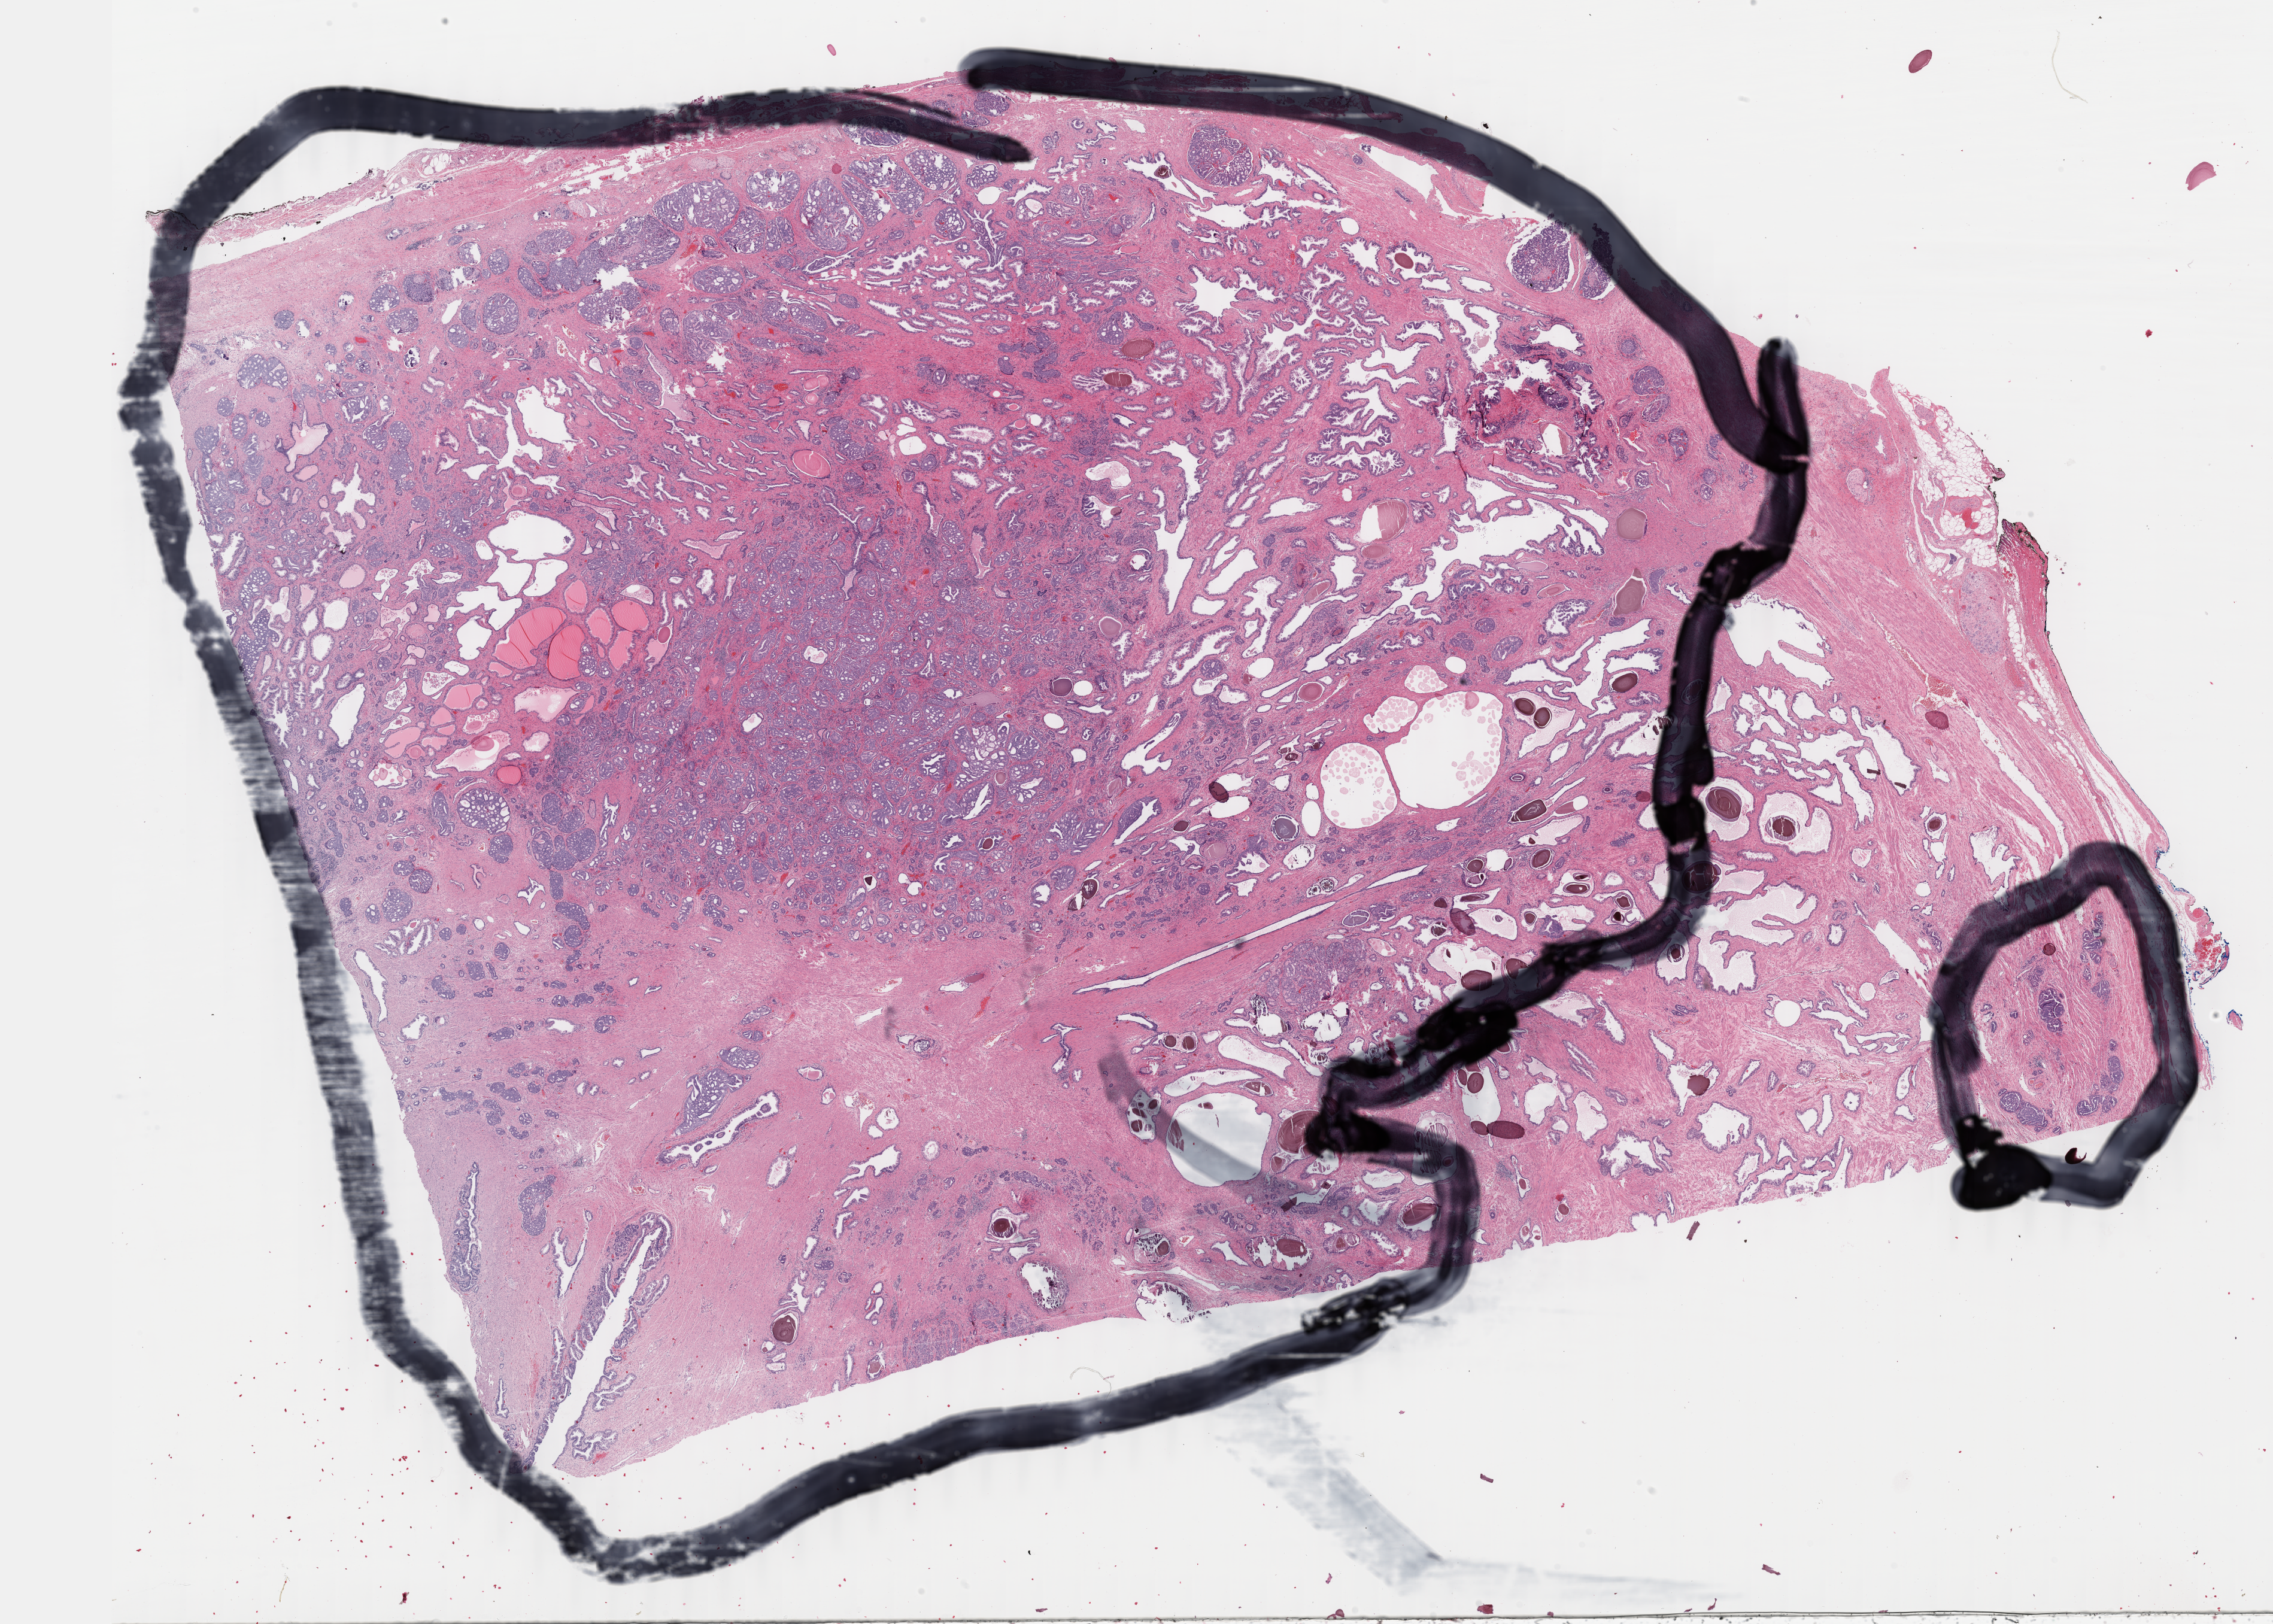
Whole-slide histology image, H&E-stained — low-resolution overview of the scanned area, about 30.2 x 21.6 mm, formalin-fixed paraffin-embedded (FFPE) diagnostic section, prostate, primary tumour sample. Patient: male, age at initial diagnosis 59 years. Gleason score: 9 (4+5).
Laterality: bilateral. Lymph nodes positive (case pathology): 0 of 1 examined. Histologic diagnosis: Adenocarcinoma, NOS.